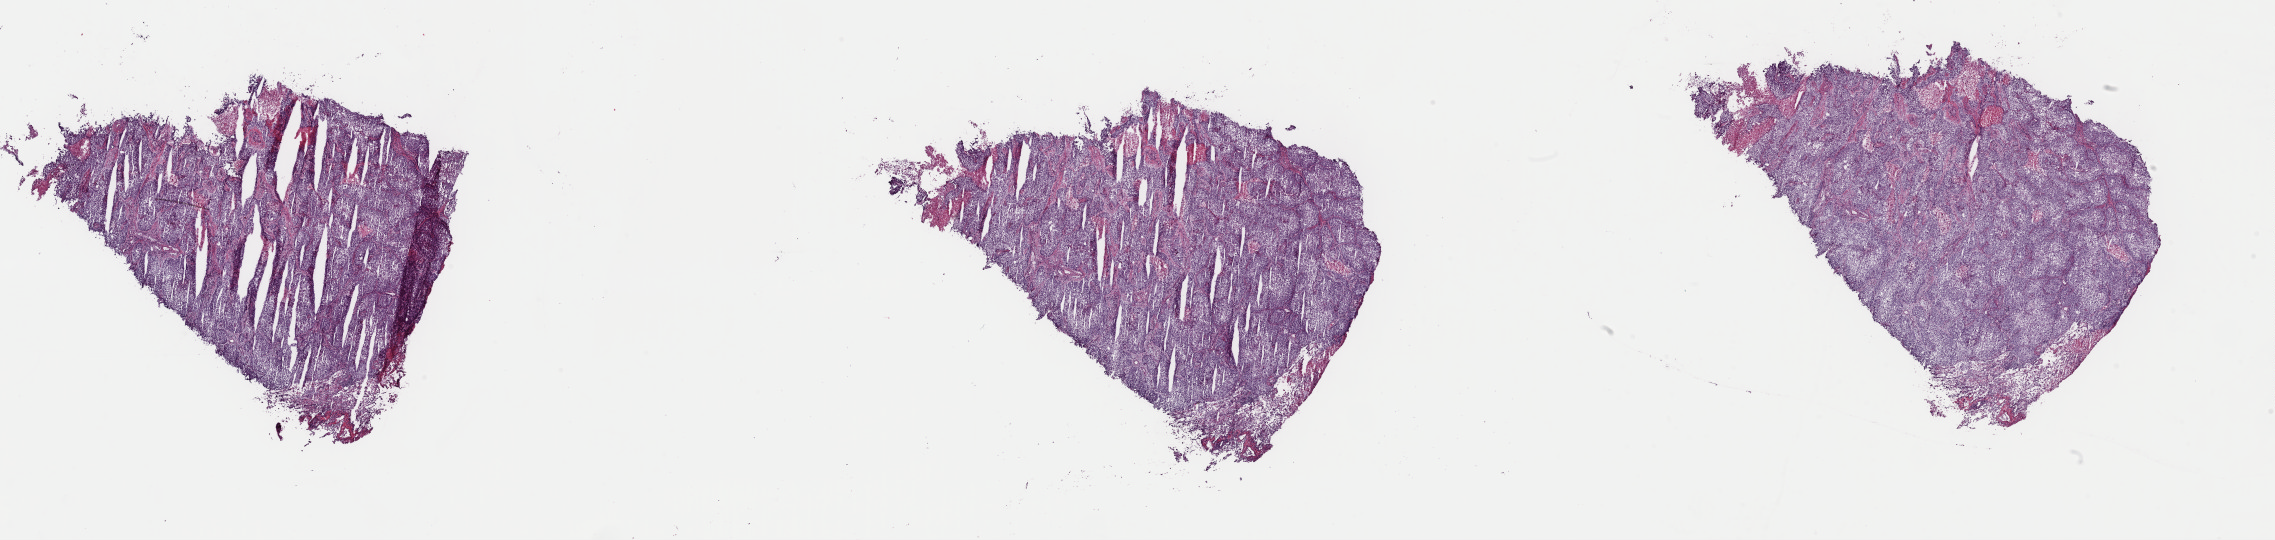
H&E whole-slide image, low-resolution overview of the scanned area, about 35.9 x 8.5 mm; frozen section; primary tumour sample from the lung. Male patient; age at initial diagnosis 70 years. Pathologist review of this section (percent, as recorded): tumour cells 80%, tumour nuclei 80%, normal cells 5%, stromal cells 5%, necrosis 10%. Inflammatory infiltration, as recorded: lymphocyte infiltration 70%, monocyte infiltration 10%, neutrophil infiltration 5%.
Histologic diagnosis: Squamous cell carcinoma, NOS (lower lobe, lung). AJCC pathologic stage: IIA.